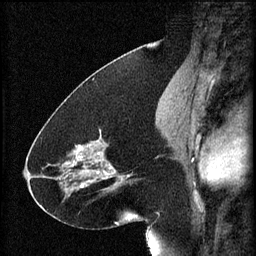
Breast MRI (dynamic contrast-enhanced), one sagittal slice. Position 31 of 60 along the scan axis. 3 images stored at this slice position (order not interpretable as contrast timing). 1.5 T. TE 4.2 ms, TR 8.2 ms. 2 mm slice thickness. 256 × 256 image matrix, field of view 180 × 180 mm. Patient: female, 41 years.
Outlined on this slice (semi-automatically segmented with operator editing):
- analysis volume of interest (the breast-tissue region the enhancement analysis was run in; not a lesion): bounding box <72,130,134,195> (left, top, right, bottom; pixels)
- tumour enhancement mask (voxels above the 70 % enhancement threshold inside the analysis volume of interest): <72,142,131,189>